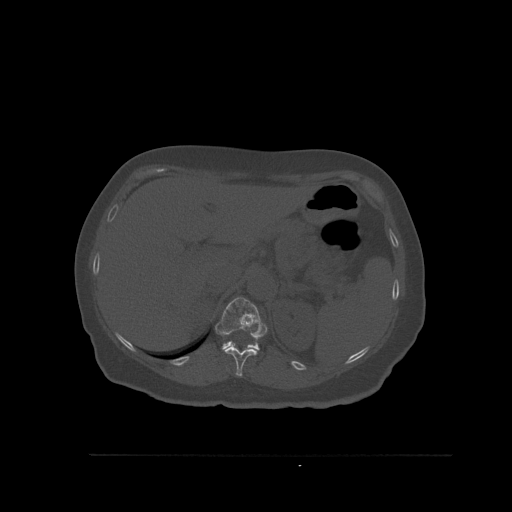
CT including the spine, one axial slice; position 294 of 527 along the scan axis; bone window (W 1800 / L 400 HU); 1.5 mm slice thickness; 512 × 512 image matrix, field of view 470 × 470 mm. Patient: female, 73 years. Case-level facts recorded for this patient, not image findings: primary cancer: breast; vertebrae with lytic lesions (as recorded): L2.
Structures marked on this image (semi-automatically segmented with operator editing):
- T11 vertebra: box from (x=223, y=347) to (x=259, y=377) px
- T12 vertebra: (x=215, y=297)–(x=267, y=350)